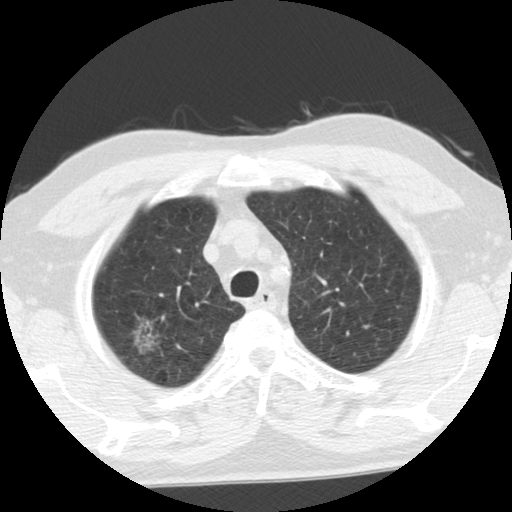
Axial slice from a low-dose chest CT screening exam, second screening round (one year after baseline), lung window (W 1500 / L -600 HU), 140 kVp. Male participant, aged 68 years at enrolment.
Expert reader's lesion annotation, bounding box [x1, y1, x2, y2] px = [129, 314, 165, 351]. The exam's reader record, not a measurement of the box and not confirmed to be the same lesion: non-calcified nodule or mass ≥4 mm, right upper lobe, poorly defined margins, ground glass attenuation, pre-existing on the prior screen: yes; interval growth: yes. Official screen result: positive, other. Lung cancer was diagnosed 88 days after this screen: adenocarcinoma, NOS, right upper lobe, moderately differentiated (G2), stage IA (AJCC 6th edition), 28 mm at pathology.